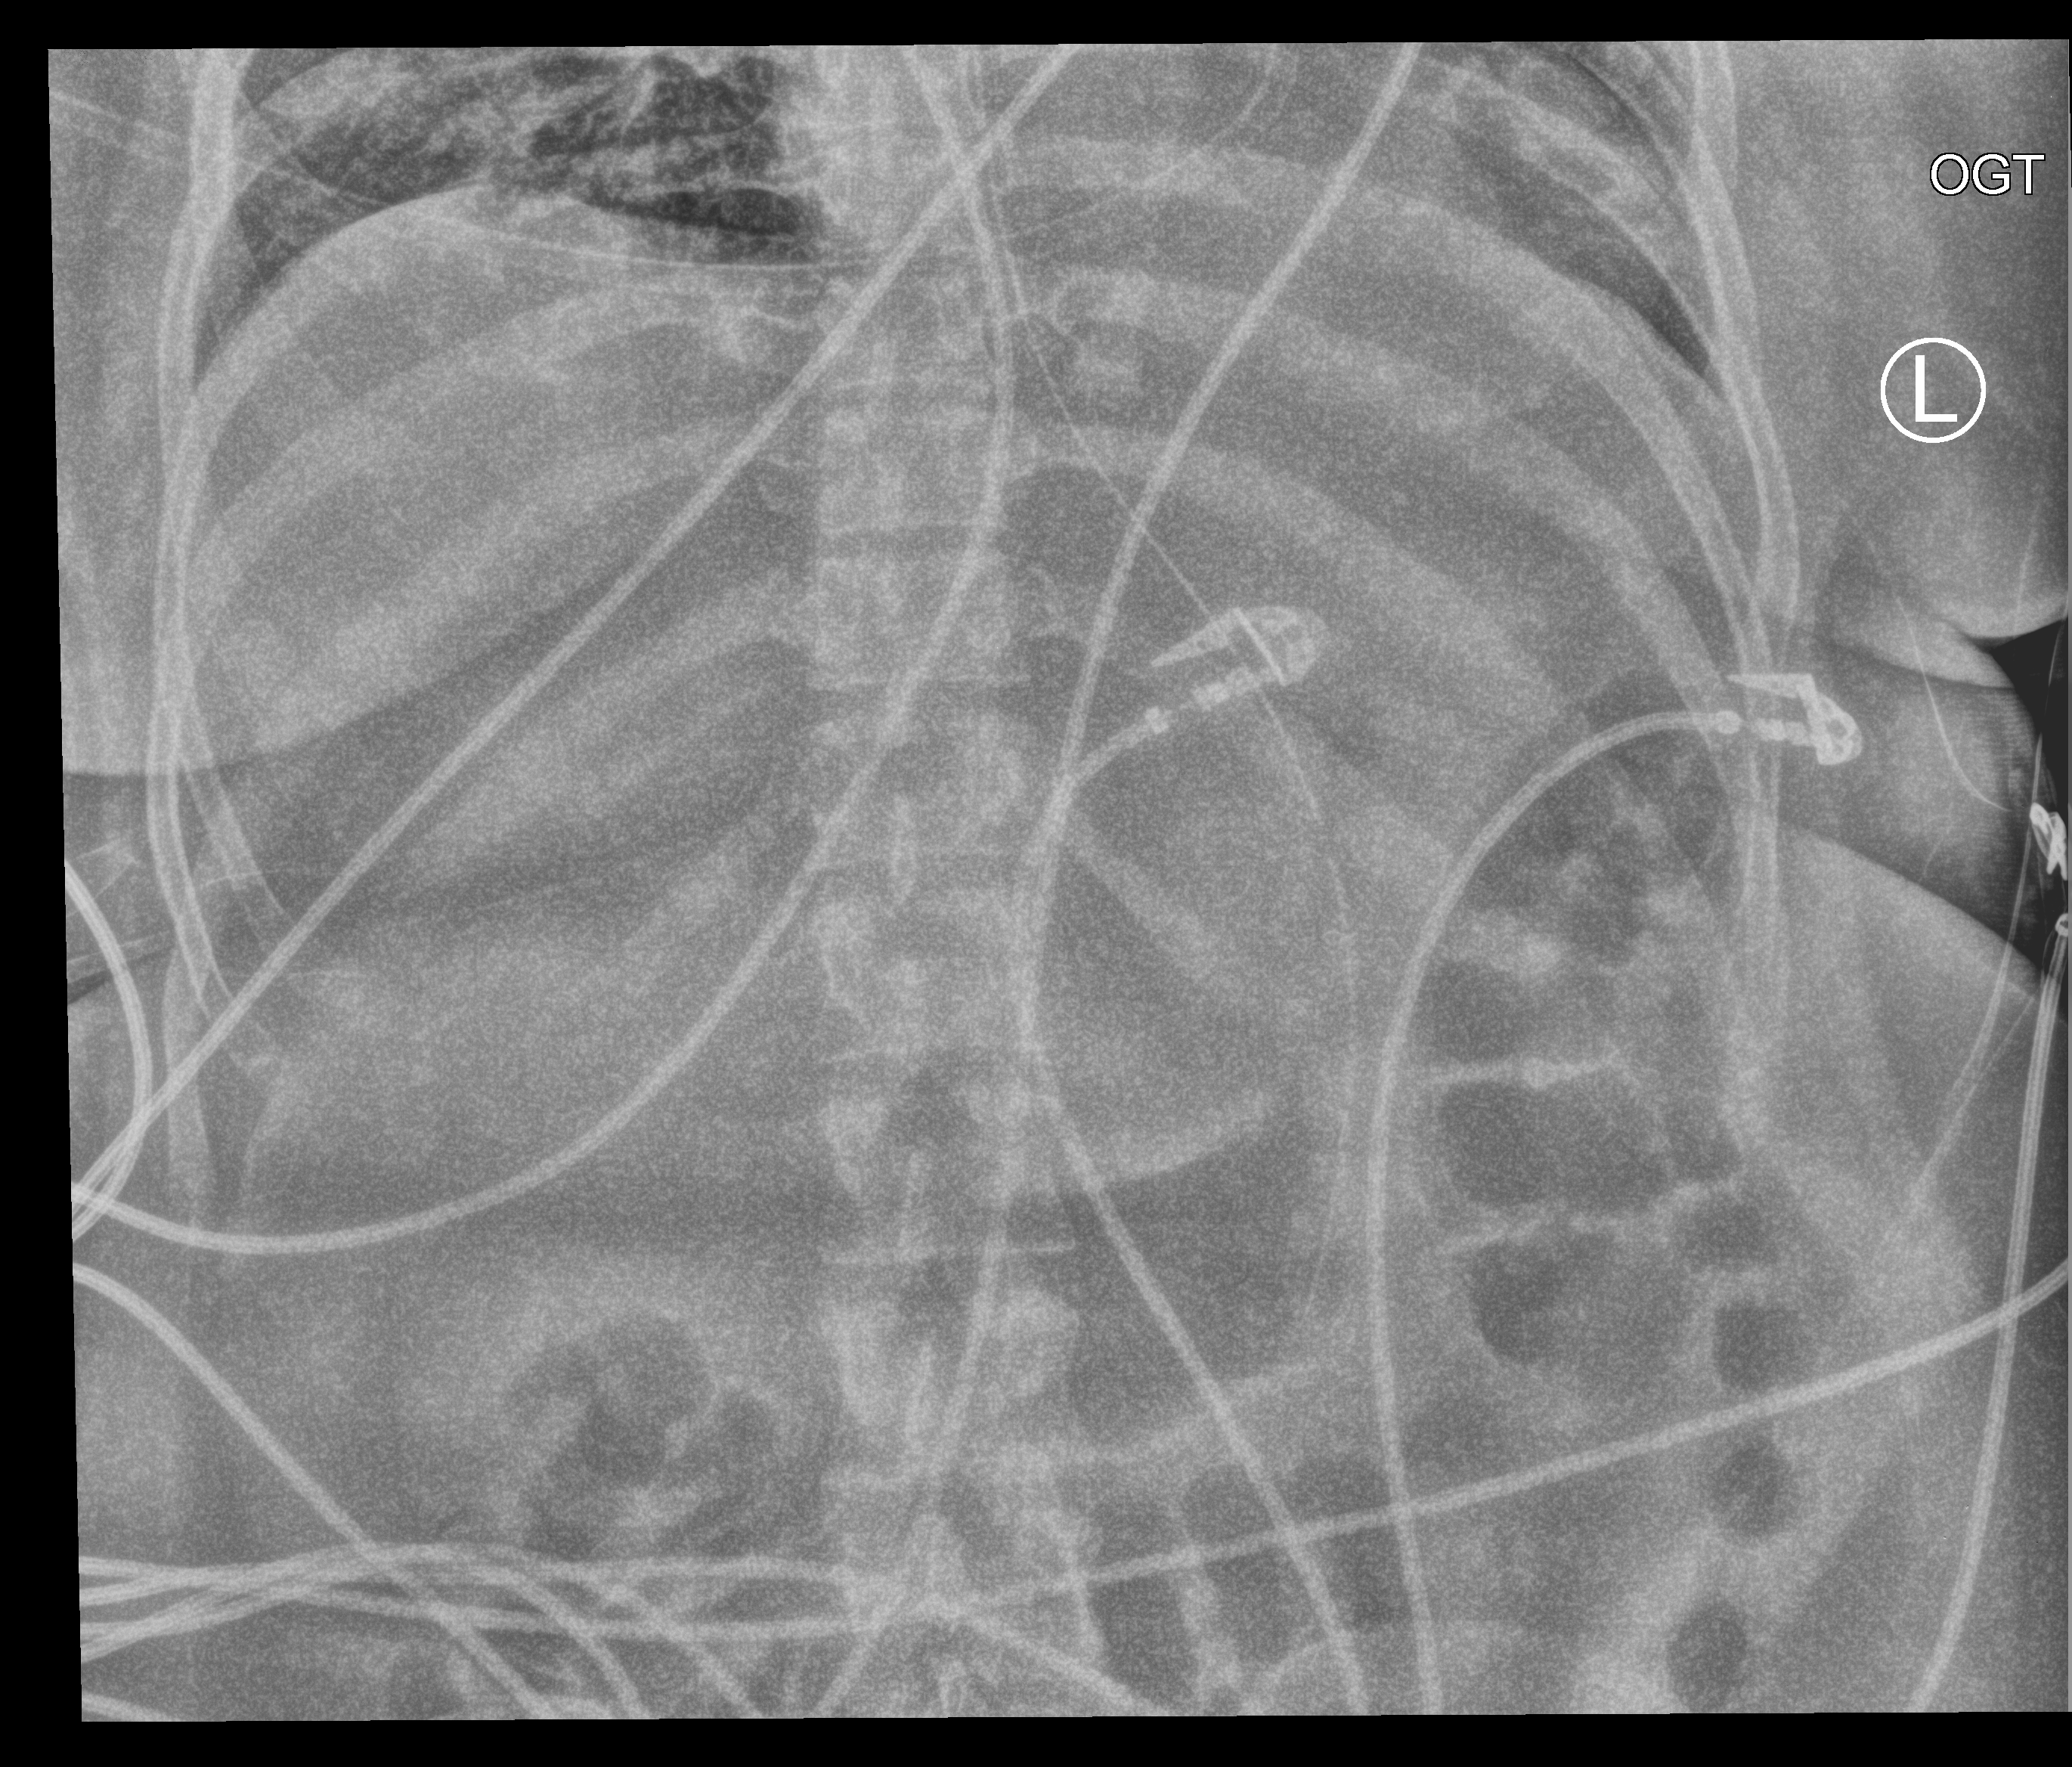
Bedside chest radiograph (computed radiography); anteroposterior (AP) projection. Female patient hospitalised with COVID-19, age 18–59 years.
Hospital-stay facts (about this admission, not read from this image; timing relative to this image not recorded): admitted to intensive care during this hospital stay: no; mechanically ventilated during this hospital stay: yes.